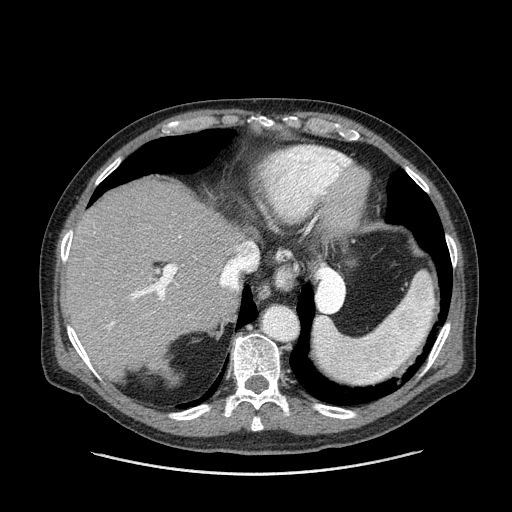
Contrast-enhanced abdominal CT (liver protocol), one axial slice. Slice 112 of 180 in the series (ordered by position). One of 2 acquisitions stored at this slice position. Soft-tissue window (W 400 / L 40 HU). 2.5 mm slice thickness. 512 × 512 image matrix, field of view 420 × 420 mm. From the clinical record (not read from this slice): diagnosis: hepatocellular carcinoma (patient treated with transarterial chemoembolisation; whether this scan precedes or follows treatment is not stated here); TNM stage (as recorded): Stage-II; Child-Pugh class: A; tumour differentiation: well differentiated; tumour nodularity: multinodular.
Structures marked on this image (semi-automatic segmentation, software-assisted and operator-edited):
- liver parenchyma outside the tumour (the mass and vessels are separate outlines, so this box may not span the whole liver): bounding box [x1, y1, x2, y2] px = [64, 180, 246, 380]
- liver vessels: [70, 240, 178, 363]